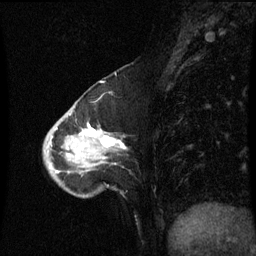
Breast MRI (dynamic contrast-enhanced), one sagittal slice. Position 22 of 60 along the scan axis. Dynamic contrast-enhanced series, image 2 of 3 at this slice position (ordered by acquisition). 1.5 T. TE 4.2 ms, TR 8.9 ms. 2 mm slice thickness. 256 × 256 image matrix, field of view 200 × 200 mm. Female patient, age 50 years. Case-level facts recorded for this patient, not image findings: setting: breast cancer imaged before/during neoadjuvant chemotherapy; receptor status: HR-positive, HER2-negative.
Annotated regions visible in this slice (semi-automatically segmented with operator editing):
- analysis volume of interest (the breast-tissue region the enhancement analysis was run in; not a lesion): bounding box <45,100,126,197> (left, top, right, bottom; pixels)
- tumour enhancement mask (voxels above the 70 % enhancement threshold inside the analysis volume of interest): <81,126,125,147>